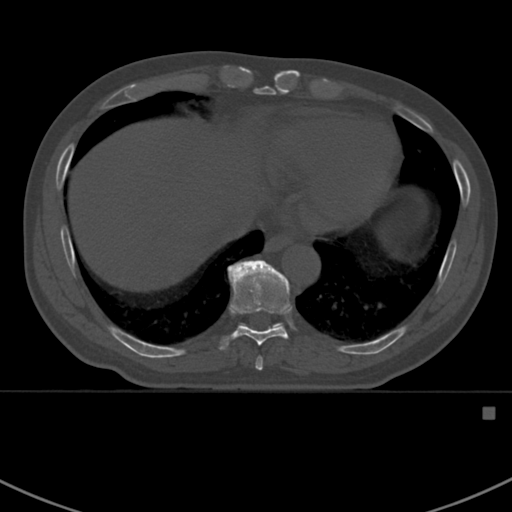
CT including the spine, one axial slice; slice 381 of 412 in the series (ordered by position); reconstruction kernel Br40s; 120 kVp; bone window (W 1800 / L 400 HU); 512 × 512 image matrix. Patient: male, 59 years. From the clinical record (not read from this slice): primary cancer: prostate.
Structures marked on this image (semi-automatic segmentation, software-assisted and operator-edited):
- T10 vertebra: bounding box (x1, y1, x2, y2) in pixels: (241, 322, 282, 327)
- T8 vertebra: (255, 357, 263, 371)
- T9 vertebra: (219, 260, 290, 350)